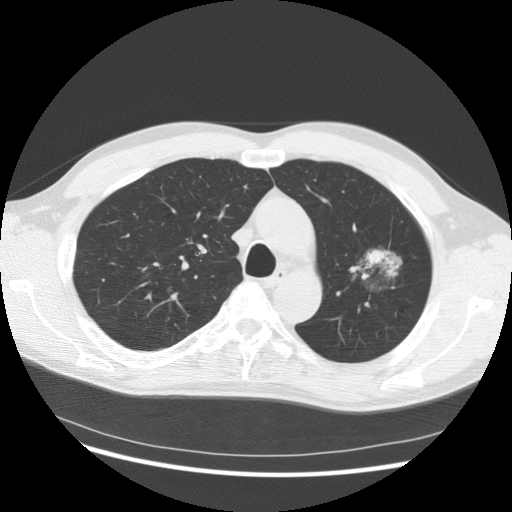
Low-dose screening chest CT, one axial slice; slice 102 of 145 in the series (ordered by position); reconstruction kernel STANDARD; lung window (W 1500 / L -600 HU); 2.5 mm slice thickness; 512 × 512 image matrix.
Outlined on this slice (manually delineated by an expert):
- lesion 1 (tumor, upper lobe of left lung): bounding box (x1, y1, x2, y2) in pixels: (367, 250, 400, 276)